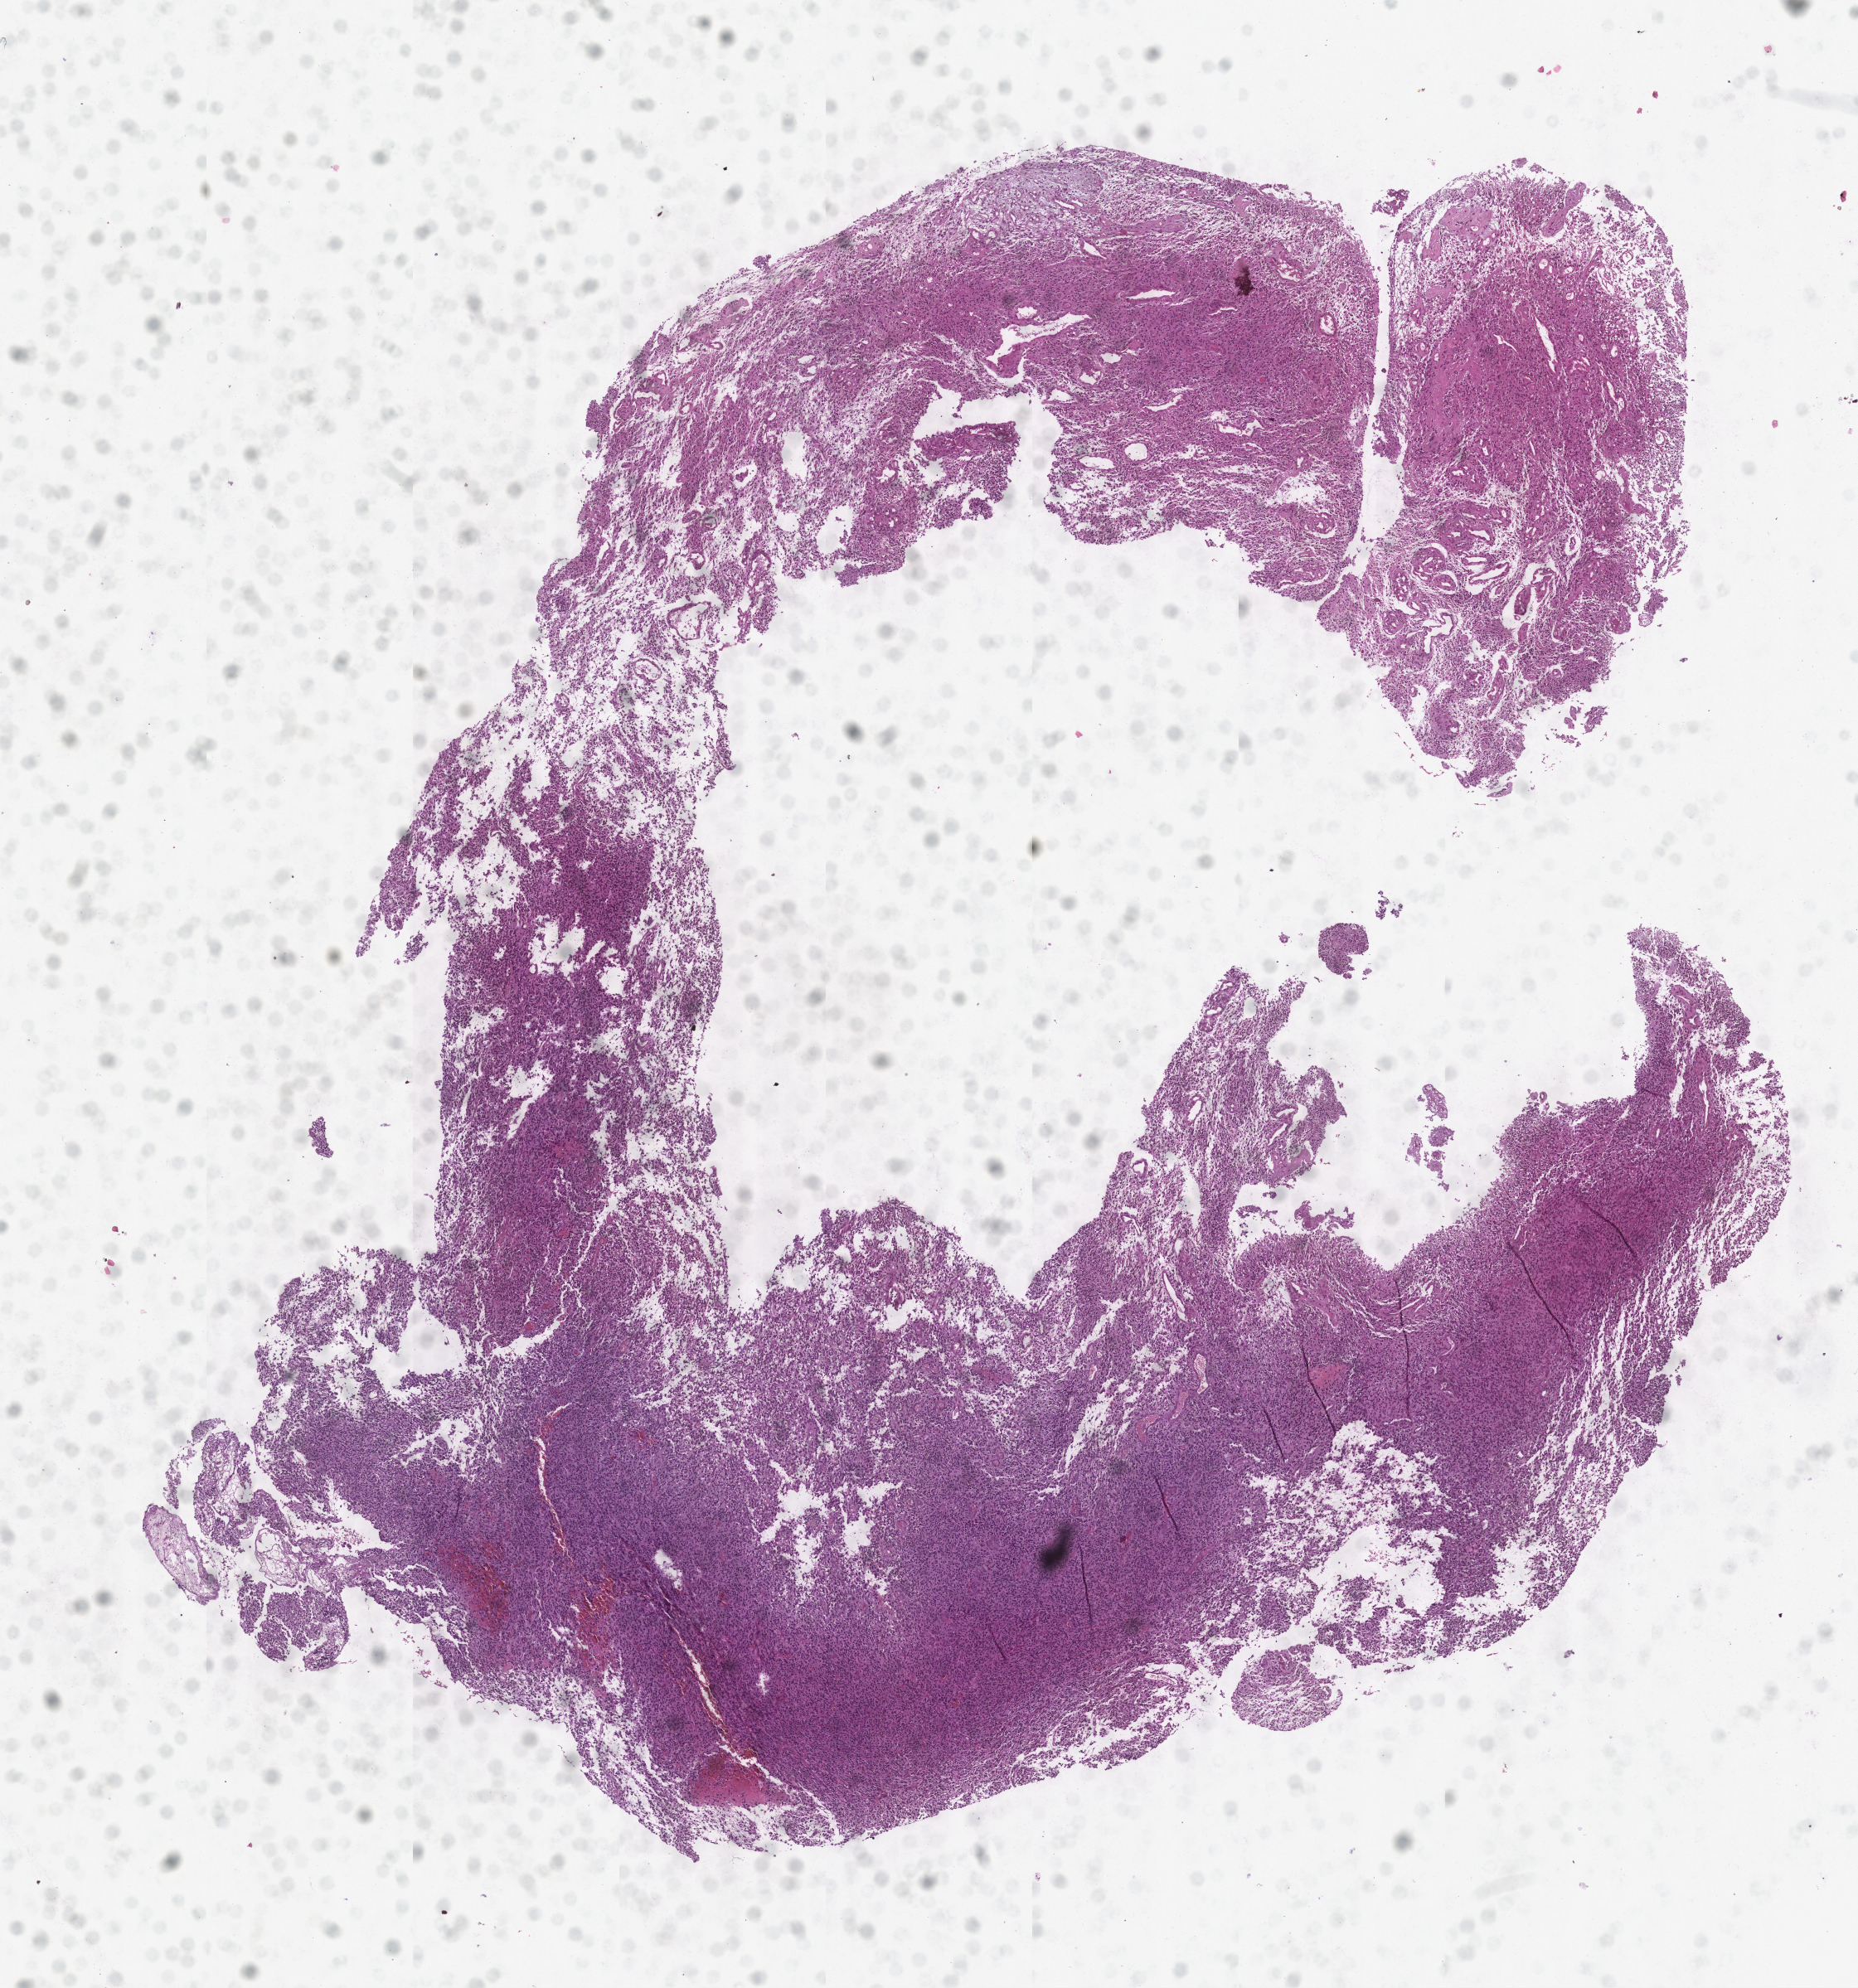
Digitized Hematoxylin and eosin (H&E) stained tissue section (whole slide) — shown as a low-resolution overview of the whole scanned area (about 9.0 x 9.7 mm, acquisition: 20x scan); tumour tissue sample, brain. Male, 71 y/o.
Histologic diagnosis: Glioblastoma.